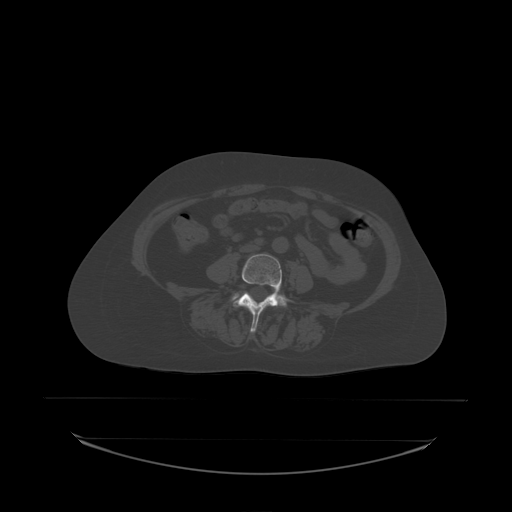
CT including the spine, one axial slice; slice 49 of 242 in the series (ordered by position); bone window (W 1800 / L 400 HU); 2.5 mm slice thickness; 512 × 512 image matrix, field of view 500 × 500 mm. Patient: female, 53 years. Case-level facts recorded for this patient, not image findings: primary cancer: lung.
Annotated regions visible in this slice (semi-automatic segmentation, software-assisted and operator-edited):
- L4 vertebra: bounding box <234,254,289,333> (left, top, right, bottom; pixels)
- L5 vertebra: <233,294,238,300>